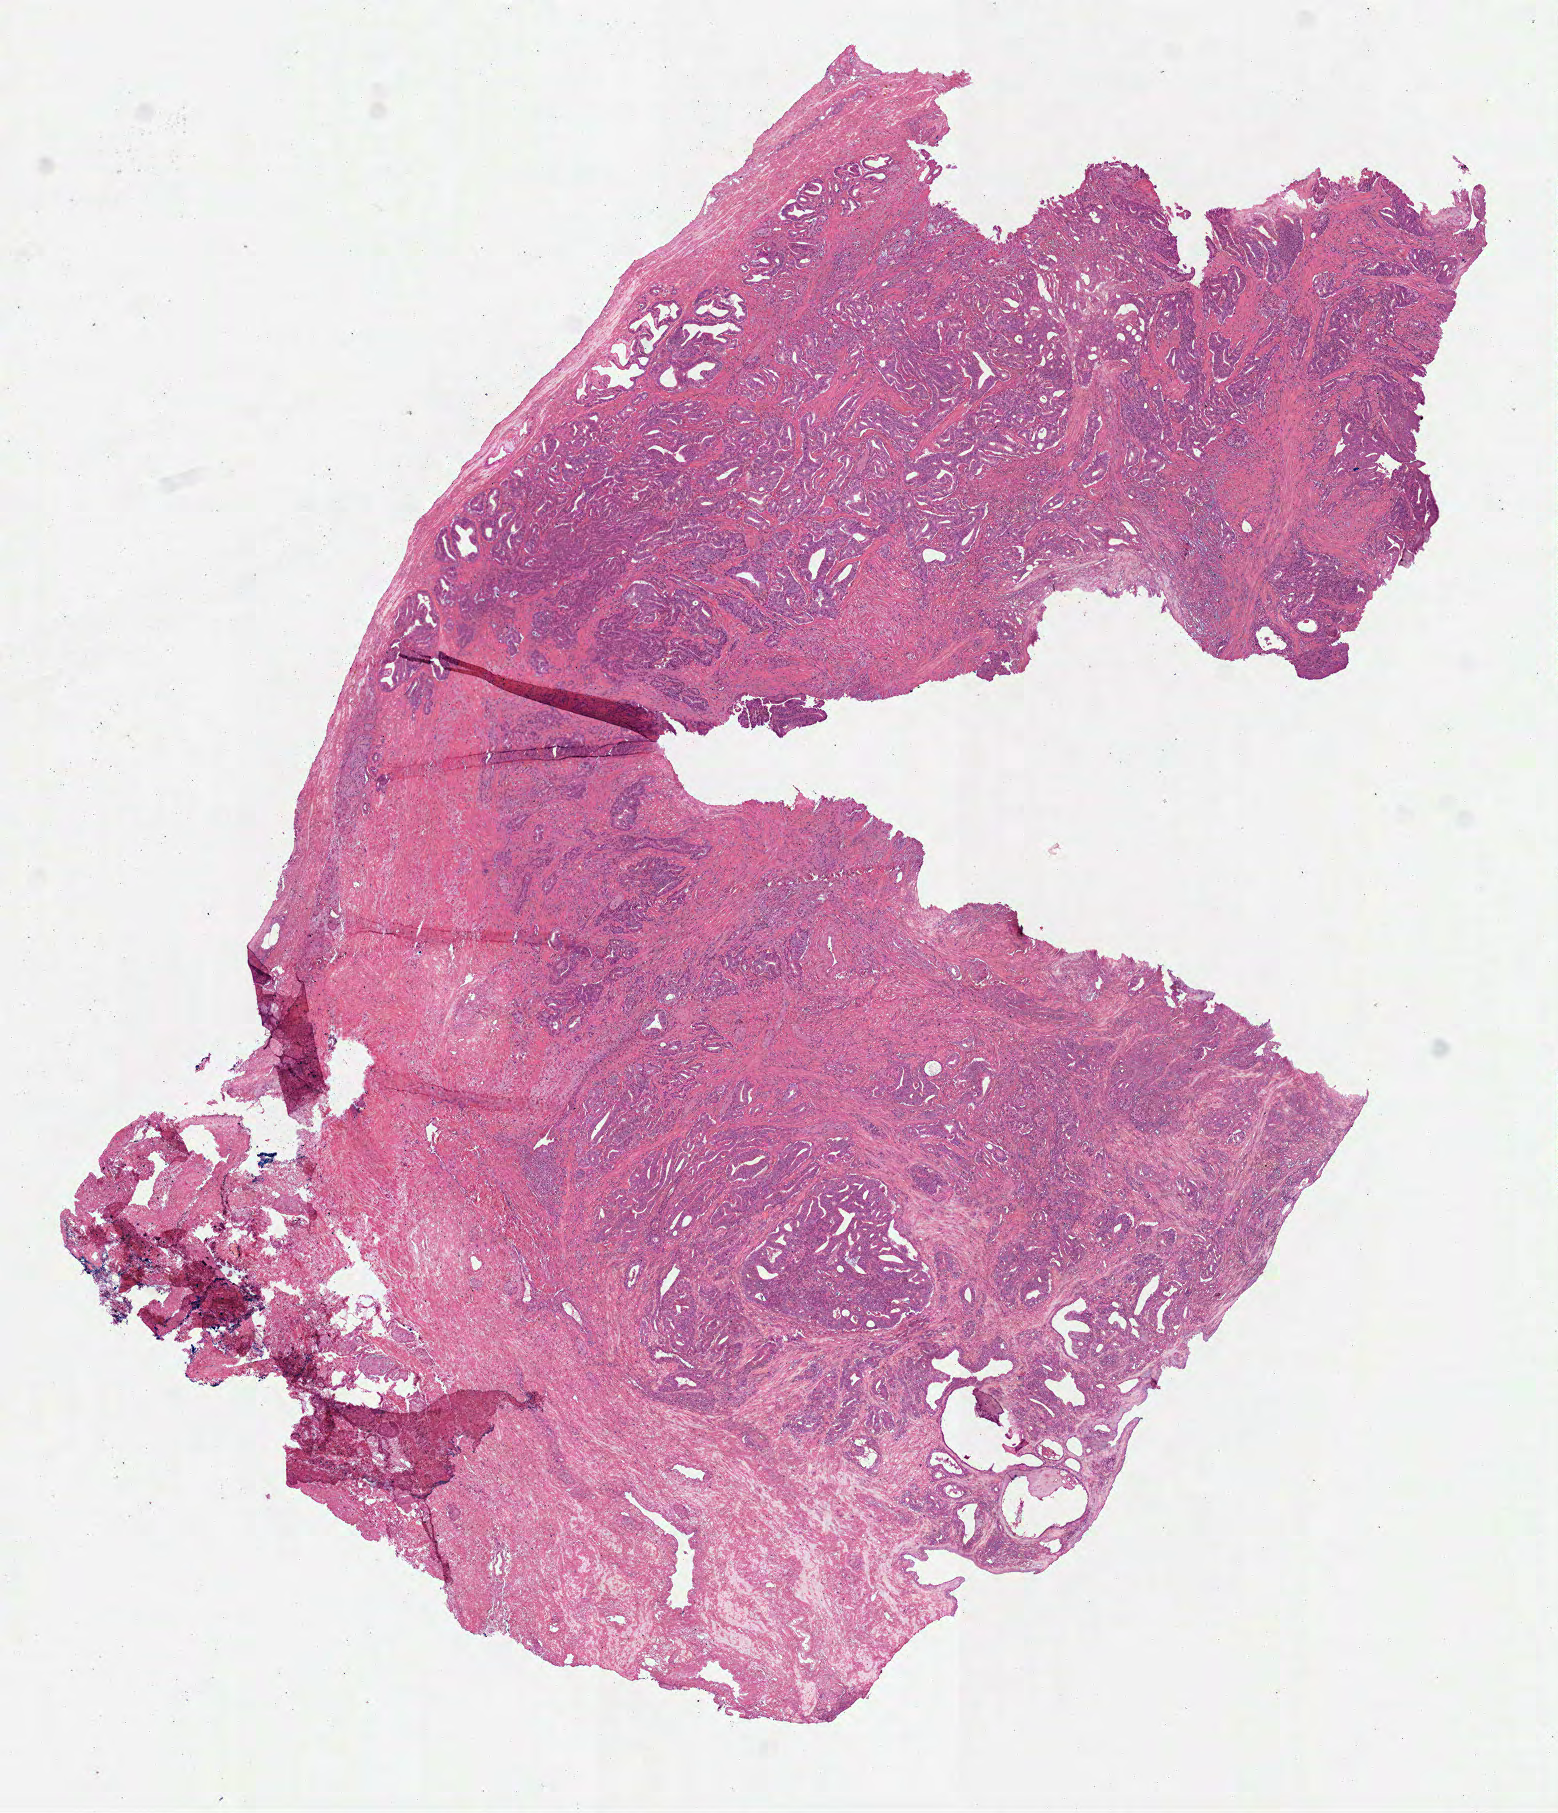
H&E whole-slide image — low-resolution overview of the scanned area, about 6.3 x 7.3 mm (slide scanned at 40x). Formalin-fixed paraffin-embedded (FFPE) diagnostic section. Primary tumour sample from the prostate. Male patient; age at initial diagnosis 57 years.
Diagnosis: Acinar cell carcinoma (prostate gland).